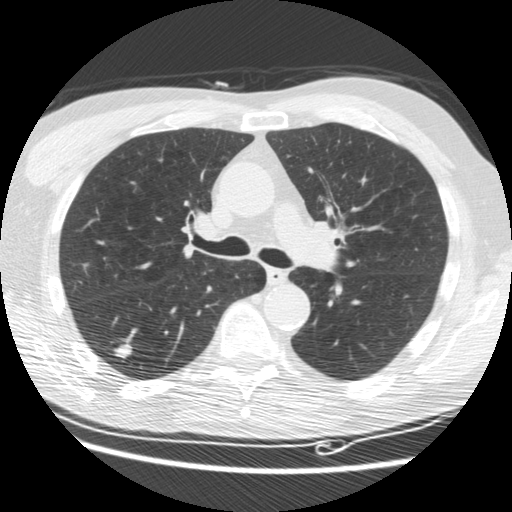
Low-dose screening chest CT, axial slice. Third screening round (two years after baseline). Lung window (W 1500 / L -600 HU). 2.5 mm slice thickness. 120 kVp. Slice 68 of 176 in the series. Male, age 62 years at enrolment. Current smoker at enrolment.
• Expert reader's lesion annotation, bounding box (x1, y1, x2, y2) in pixels: (99, 332, 143, 371).
• The screening reader recorded 3 non-calcified nodules or masses ≥4 mm on this exam (right lower lobe, right lower lobe, right lower lobe); which of them this box marks is not recorded.
• Official screen result: positive, other.